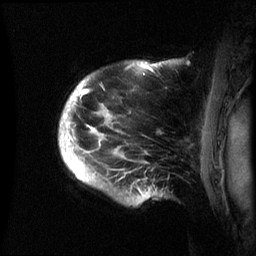
Breast MRI (dynamic contrast-enhanced), one sagittal slice. Slice 52 of 60 in the series (ordered by position). Dynamic contrast-enhanced series, image 2 of 3 at this slice position (ordered by acquisition). 1.5 T. TE 4.2 ms, TR 8.4 ms. 256 × 256 image matrix. Patient: female, 48 years.
Outlined on this slice (semi-automatic segmentation, software-assisted and operator-edited):
- analysis volume of interest (the breast-tissue region the enhancement analysis was run in; not a lesion): bounding box <59,61,176,205> (left, top, right, bottom; pixels)
- tumour enhancement mask (voxels above the 70 % enhancement threshold inside the analysis volume of interest): <61,63,156,194>